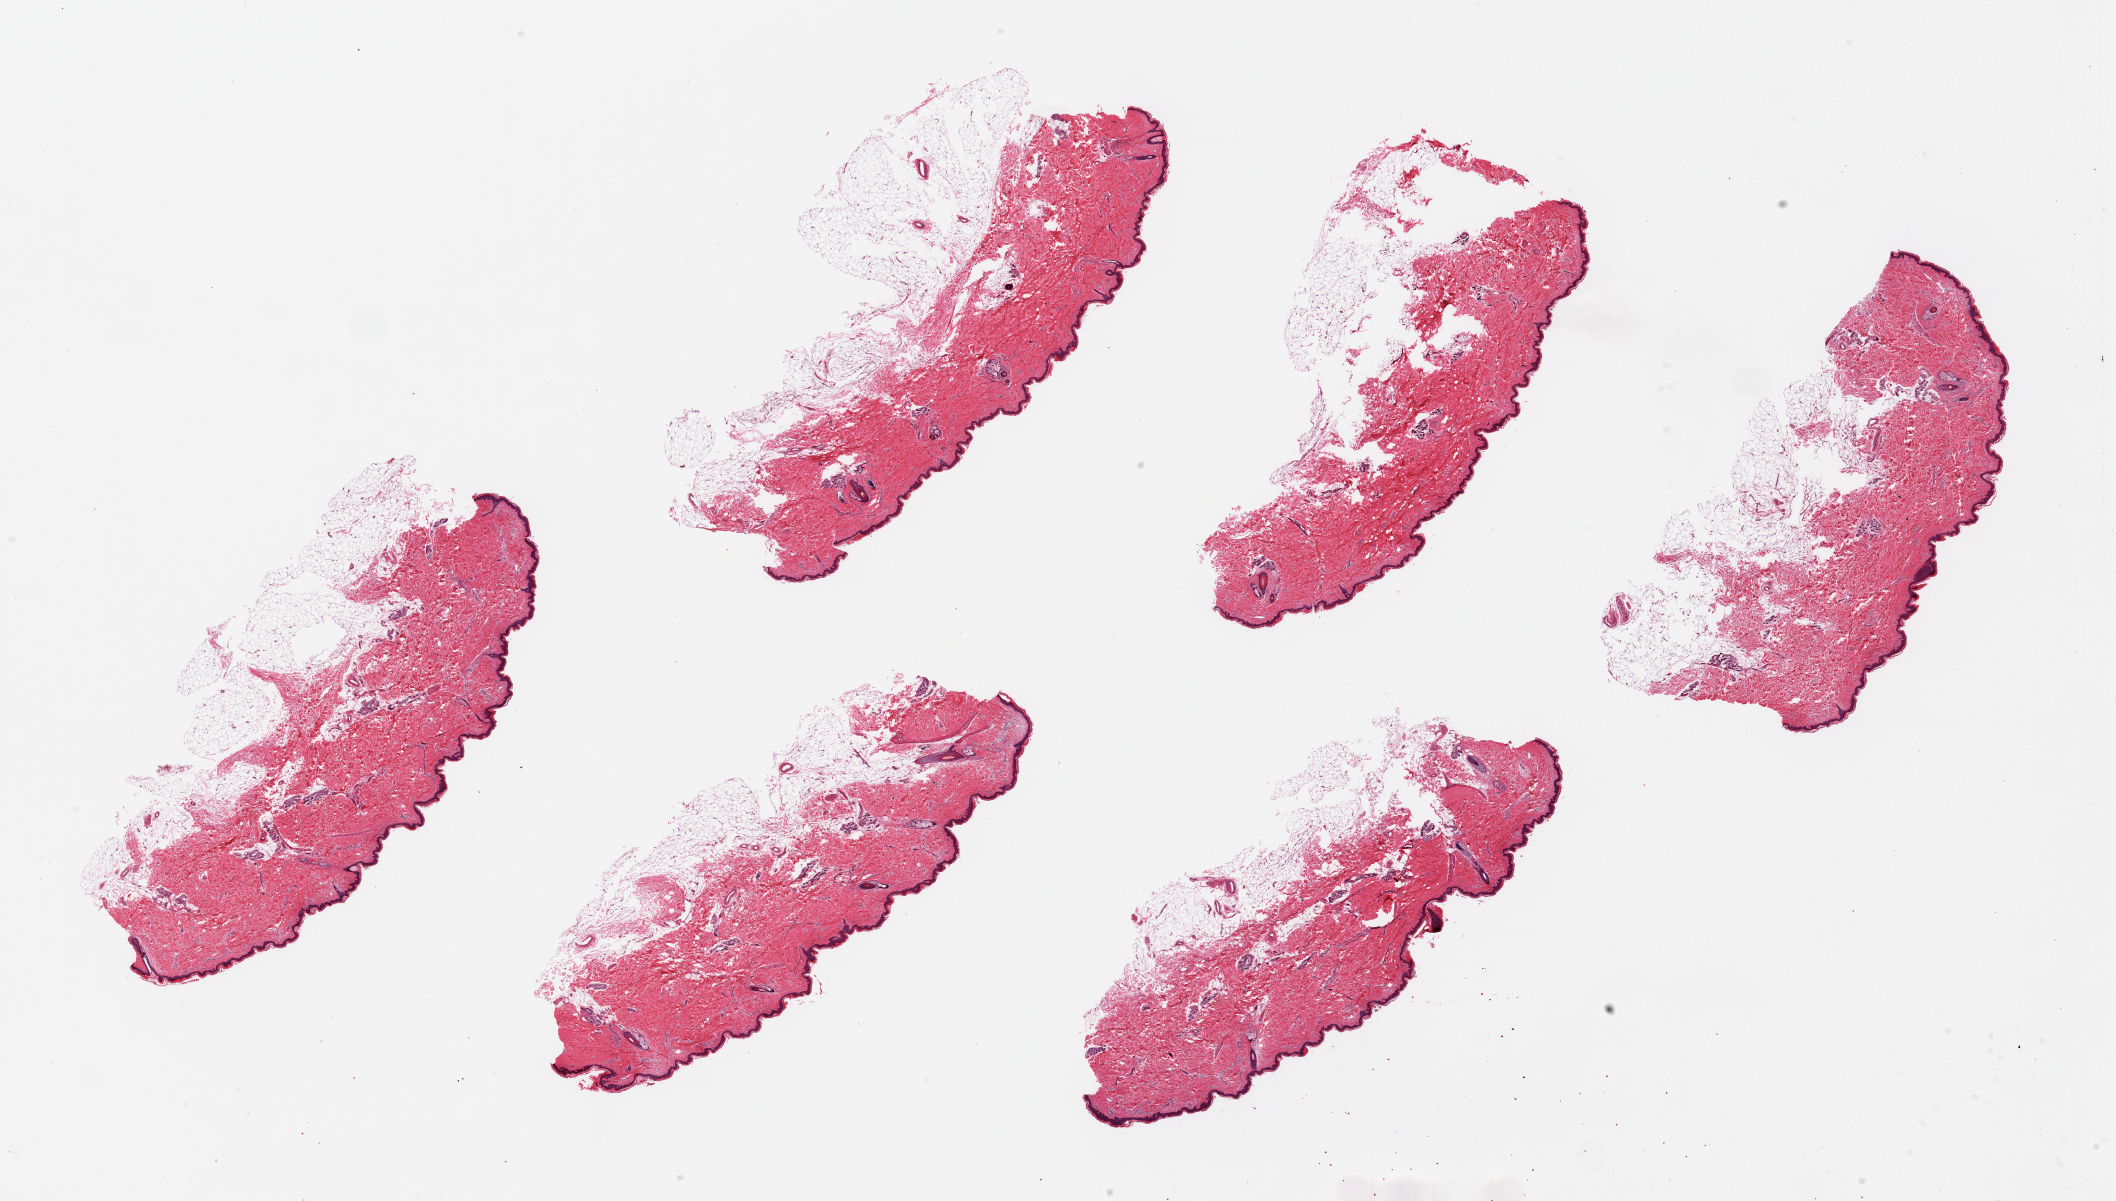
Digitized H&E-stained section — whole scanned area (about 33.5 x 19.0 mm) shown as a low-resolution overview; PAXgene-fixed paraffin-embedded (PFPE) section; sampled site (target tissue): skin of lower leg; tissue donor sample. Donor sex: female.
Pathologist's review note for this sample: 6 pieces up to 9x4.5 mm; subcutaneous fat is up to 2.5 mm thick.